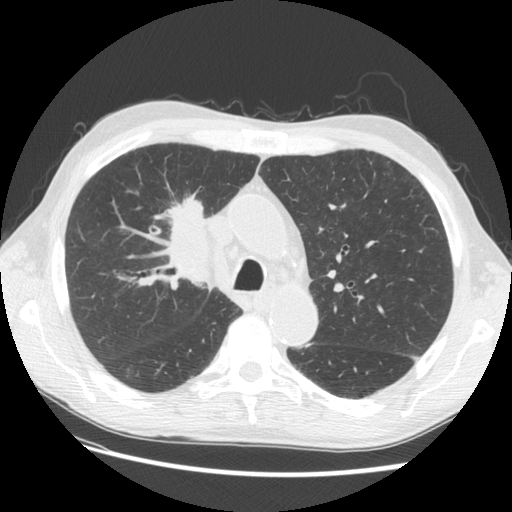
Chest CT (low-dose screening protocol), one axial image. Third screening round (two years after baseline). Lung window (W 1500 / L -600 HU). 2.5 mm slice thickness. Standard (soft-tissue) reconstruction kernel (STANDARD). Male participant, aged 73 years at enrolment. Current smoker at enrolment.
Lesion marked by an expert reader, bounding box [x1, y1, x2, y2] px = [141, 185, 233, 276]. The screening reader recorded 4 non-calcified nodules or masses ≥4 mm on this exam (right upper lobe, right upper lobe, right upper lobe, left lower lobe); which of them this box marks is not recorded. Participant outcome: lung cancer diagnosed 48 days after this screen — squamous cell carcinoma, NOS, right upper lobe, poorly differentiated (G3), stage IIIB (AJCC 6th edition), 56 mm at pathology.